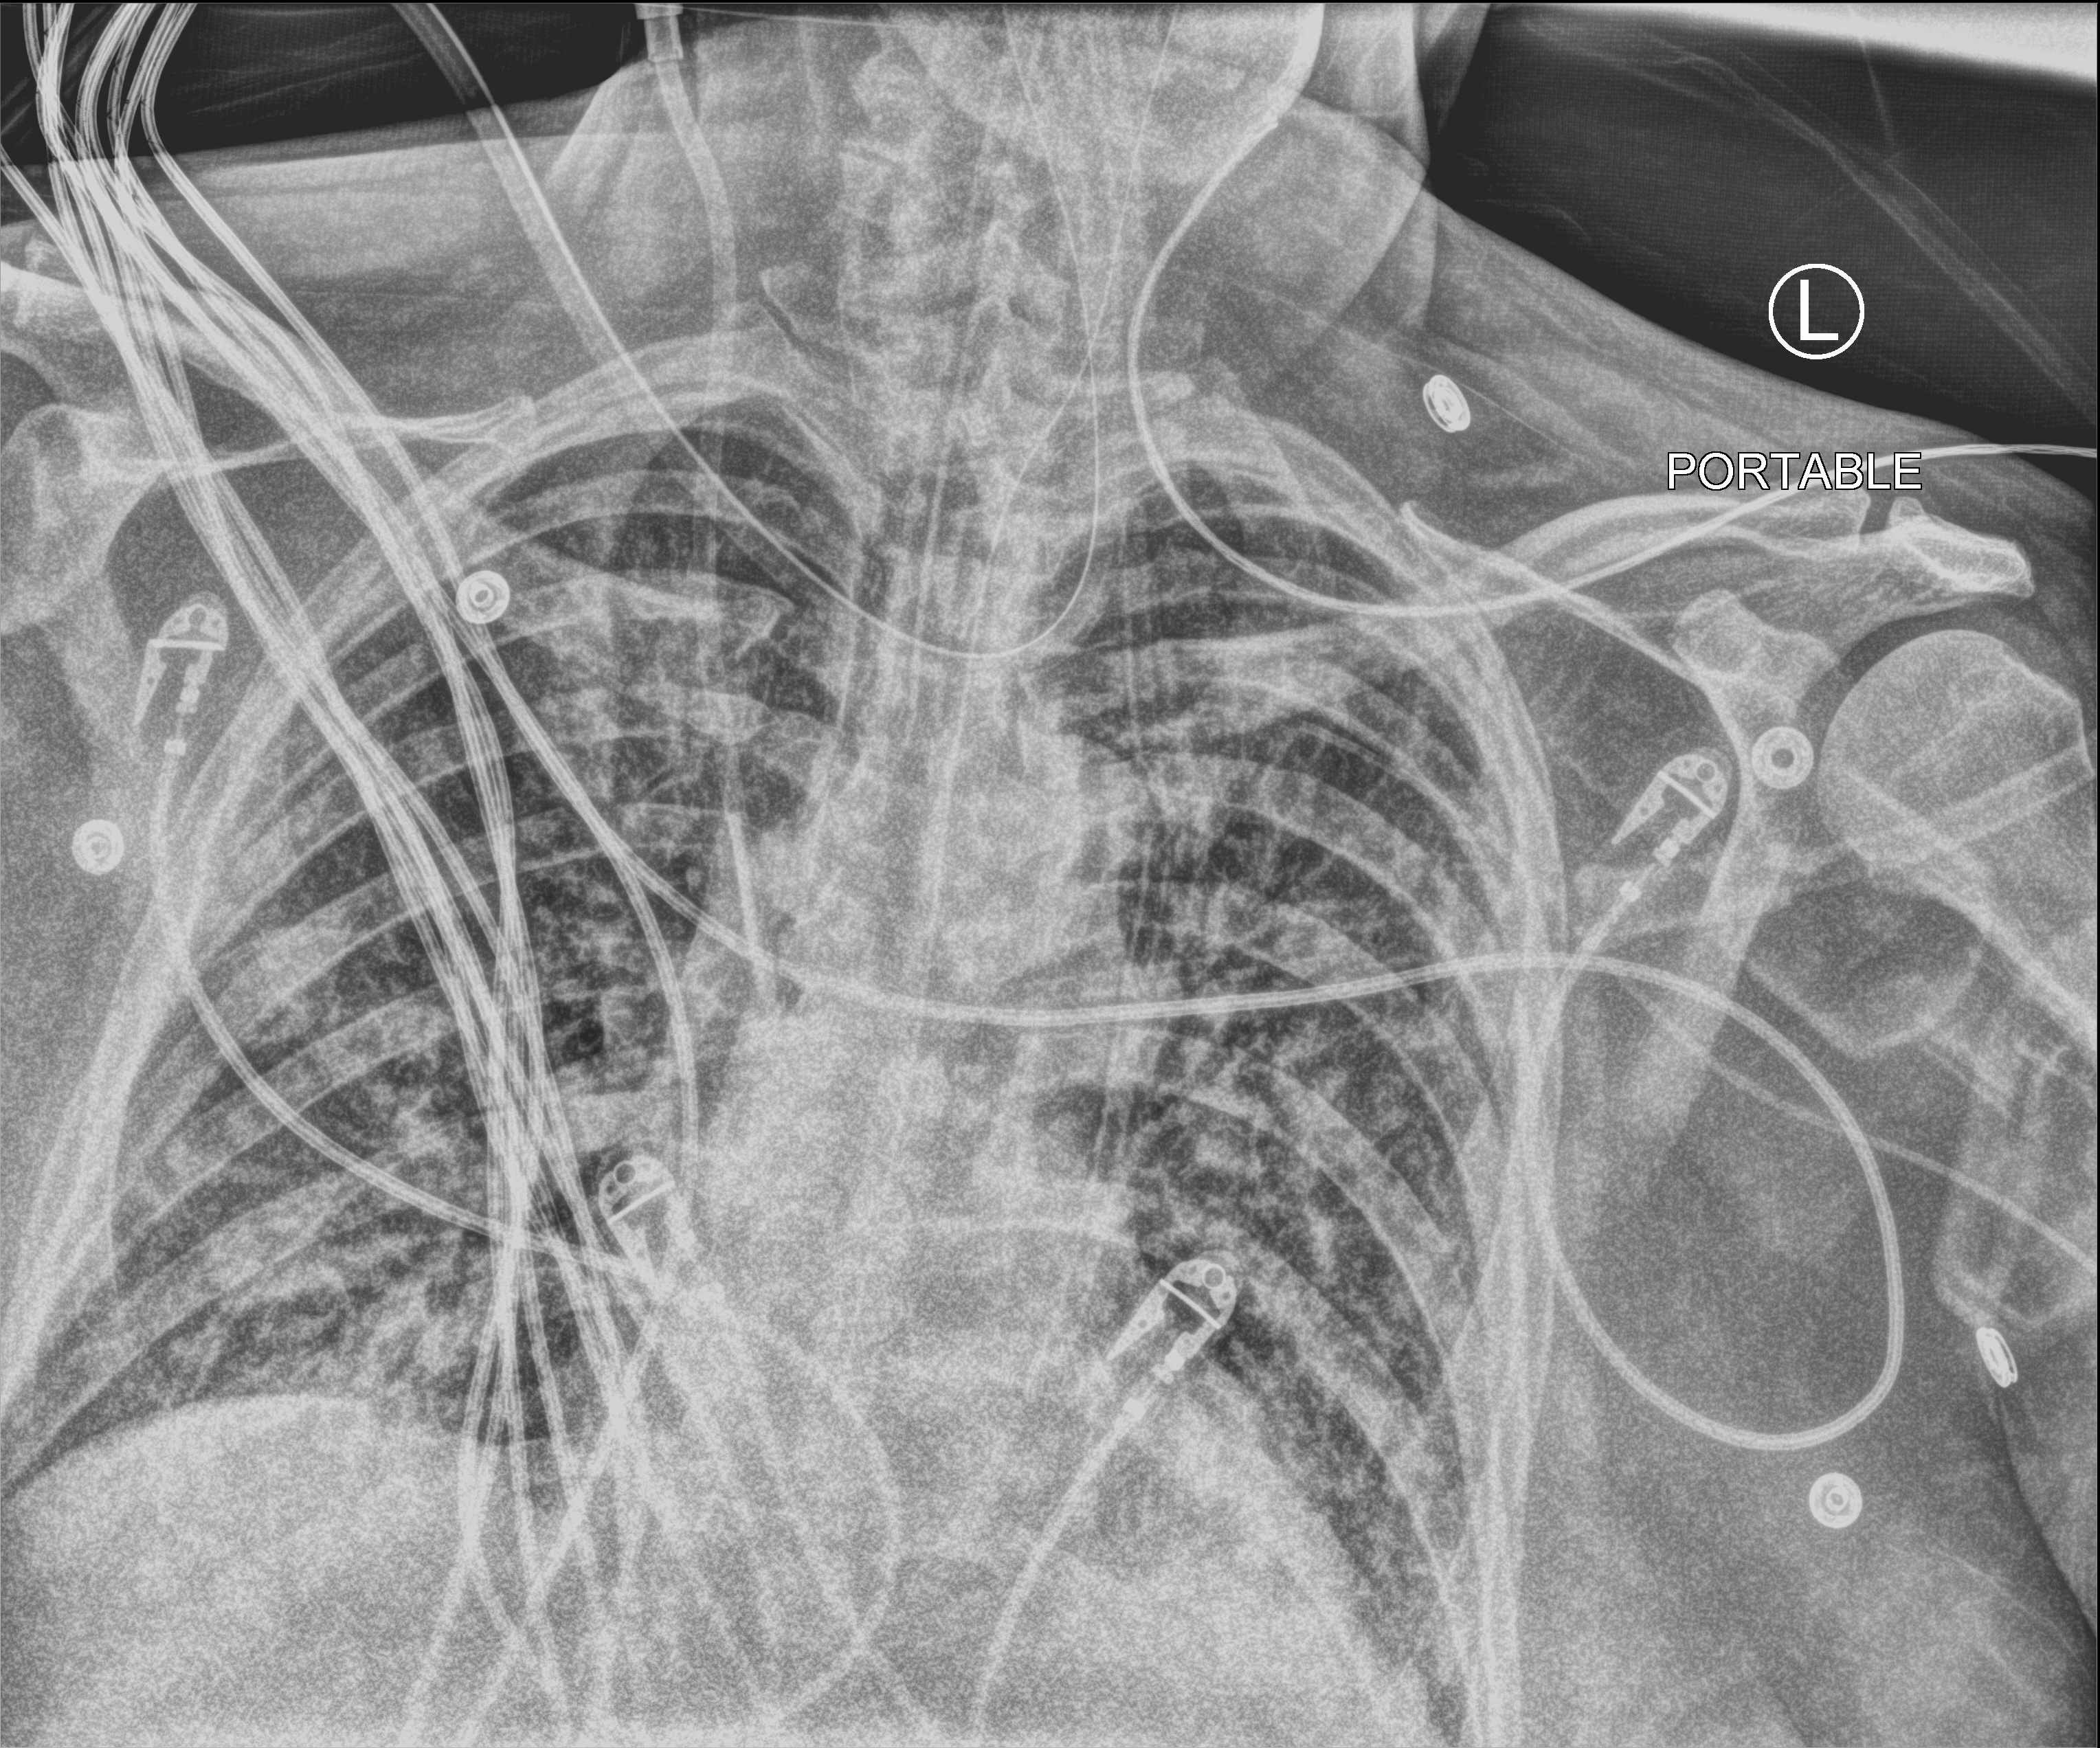
Chest X-ray (portable). Patient hospitalised with COVID-19; male, aged 60–74 years.
Admission-level facts for this patient (not findings on this image; timing relative to this image not recorded):
- mechanically ventilated during this hospital stay: yes
- admitted to intensive care during this hospital stay: yes
- diabetes (admission record): no